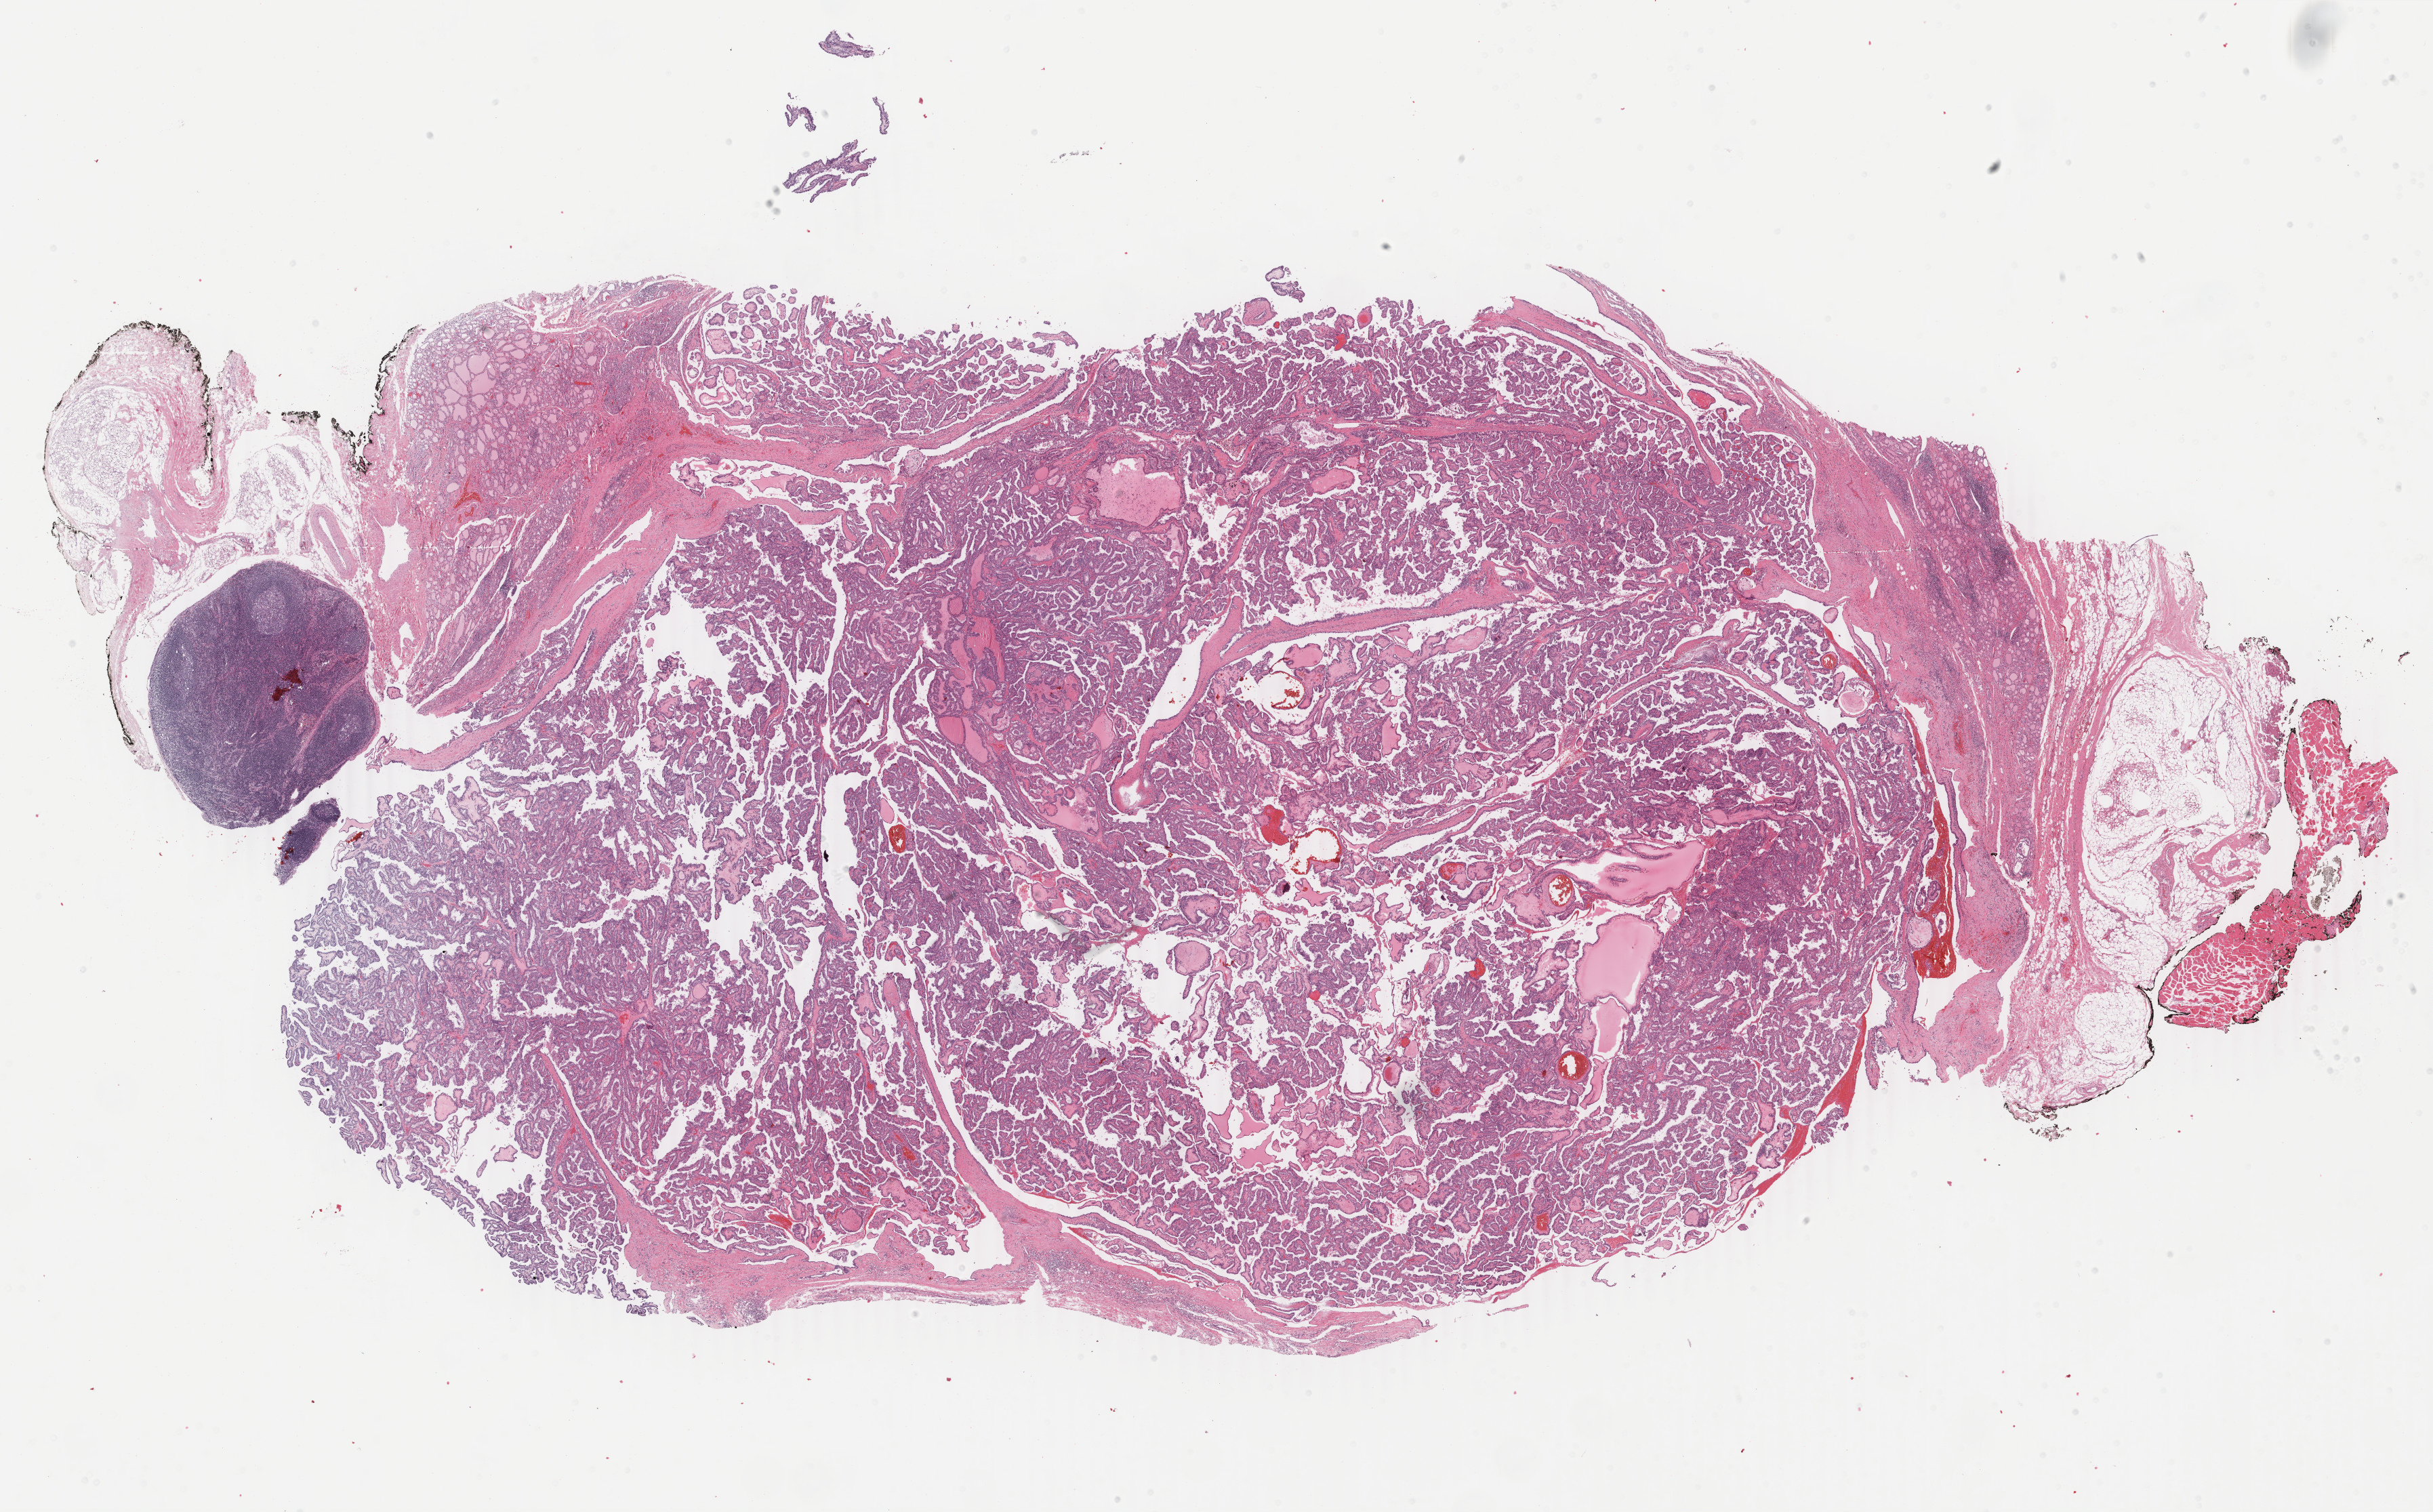
Digitized Hematoxylin and eosin (H&E) stained tissue section (whole slide), a low-resolution overview of the entire scanned area, about 28.6 x 17.7 mm. Formalin-fixed paraffin-embedded (FFPE) diagnostic section. Primary tumour sample from the thyroid. Patient: female, age at initial diagnosis 26 years.
TNM: T2 N1 MX. Laterality: midline. Diagnosis: Papillary adenocarcinoma, NOS (thyroid gland). AJCC pathologic stage: I (5th edition). Lymph nodes positive (case pathology): 3 of 4 examined.